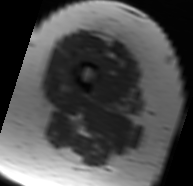
MRI of an extremity soft-tissue mass, one axial slice. MR volume resampled by the dataset authors to the PET/CT grid (not the native acquisition matrix). 3.27 mm slice thickness. 193 × 186 image matrix, field of view 188 × 182 mm. Female patient. From the clinical record (not read from this slice): histological type: malignant solitary fibrous tumor; grade: intermediate; site of the primary tumour: right thigh.
Structures marked on this image (expert contour drawn on MRI and transferred to this co-registered scan by the dataset authors):
- gross tumour volume including surrounding oedema: bounding box <109,52,112,54> (left, top, right, bottom; pixels)